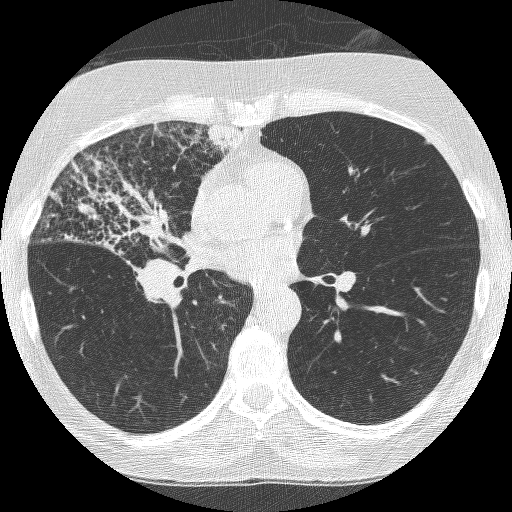
Chest CT (low-dose screening protocol), one axial image, third annual screen, lung window (W 1500 / L -600 HU), 1.25 mm slice thickness. Female participant, aged 64 years at enrolment. Former smoker at enrolment.
- Expert reader's lesion annotation, bounding box <59,167,201,311> (left, top, right, bottom; pixels).
- The exam's reader record, not a measurement of the box and not confirmed to be the same lesion: non-calcified nodule or mass ≥4 mm, right upper lobe, 49 × 43 mm, spiculated (stellate) margins, soft tissue attenuation, pre-existing on the prior screen: yes; interval growth: yes.
- Official screen result: positive, other.